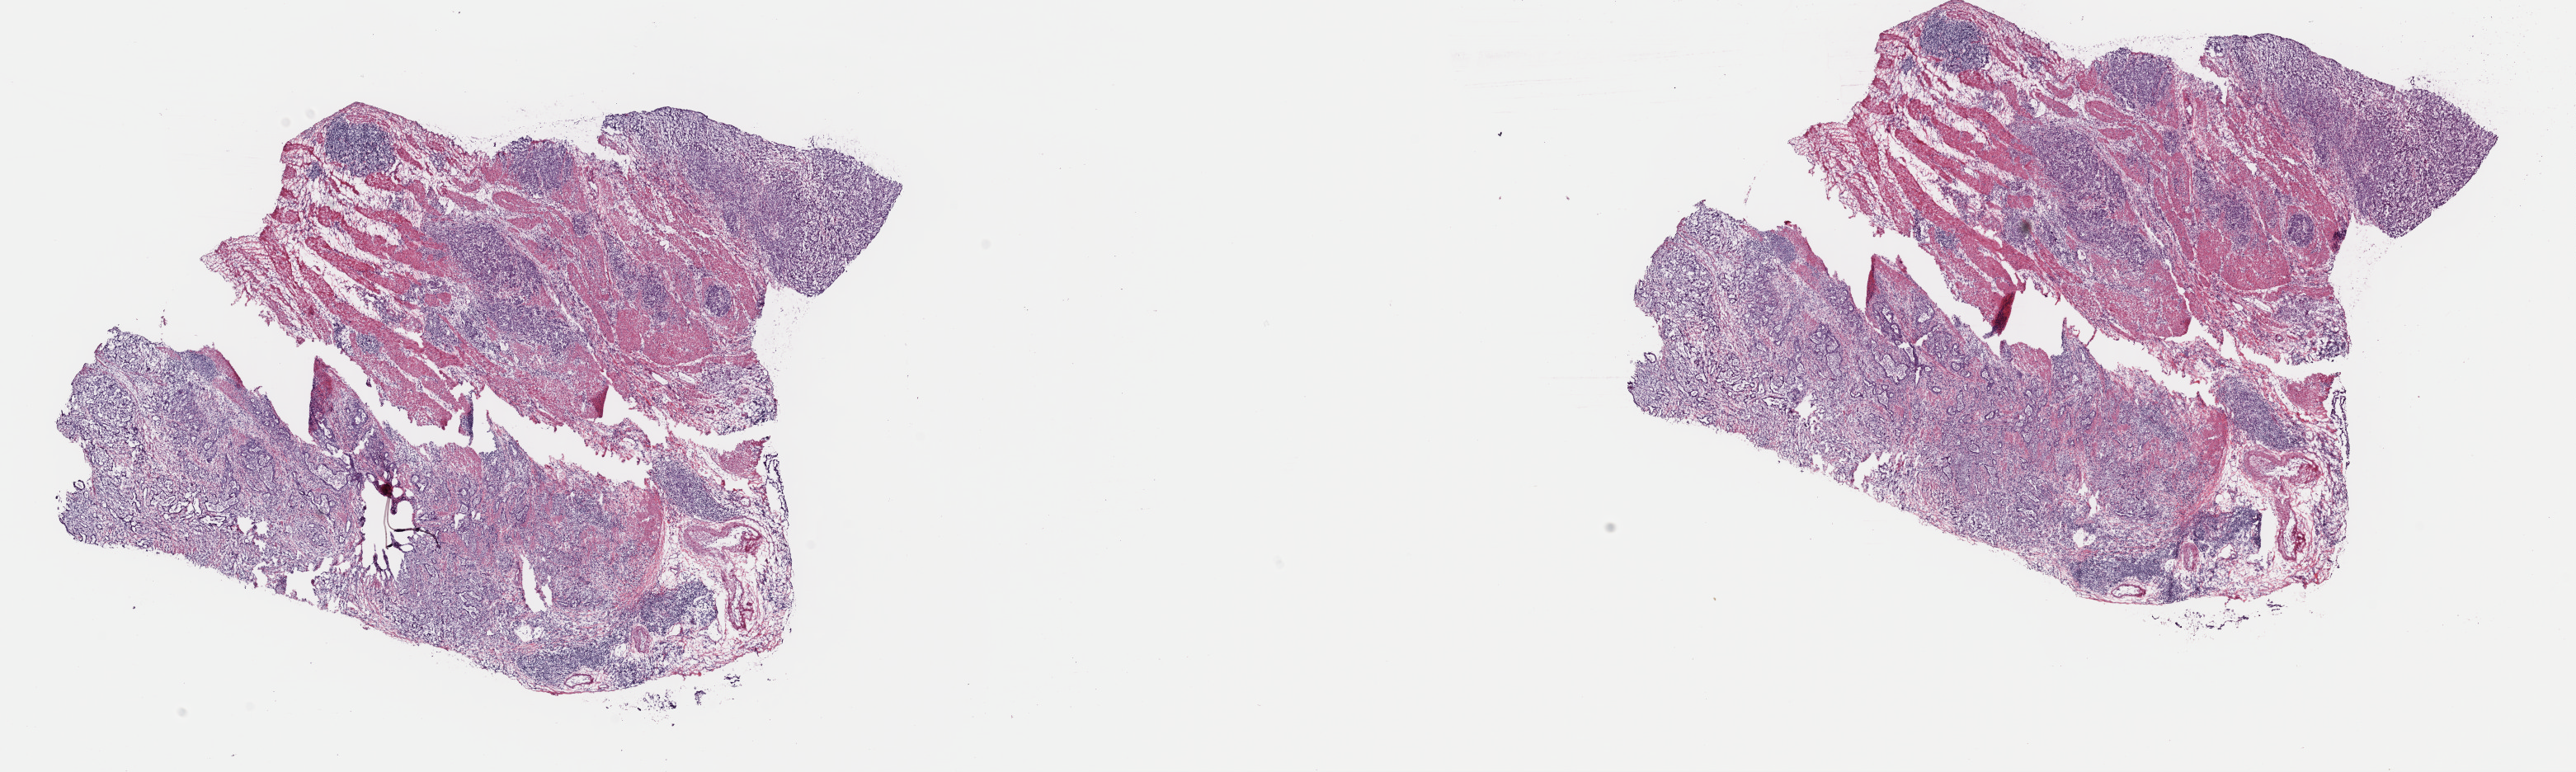
Whole-slide histology image, H&E, shown as a low-resolution overview of the whole scanned area (about 24.7 x 7.4 mm, acquisition: 40x scan). Frozen section from the top of the tissue portion. Sample: primary tumour, stomach. Patient: female, age at initial diagnosis 72 years. Histologic grade: G3 (poorly differentiated). Composition of this section per pathologist review: tumour cells 60%, tumour nuclei 70%, normal cells 10%, stromal cells 30%, necrosis 0%. Inflammatory infiltration, as recorded: lymphocyte infiltration 0%, monocyte infiltration 0%, neutrophil infiltration 0%.
Lymph nodes positive (case pathology): 13 of 18 examined. Pathologic diagnosis: Tubular adenocarcinoma (gastric antrum). AJCC pathologic stage: IIIB (7th edition). TNM: T3 N3a M0.